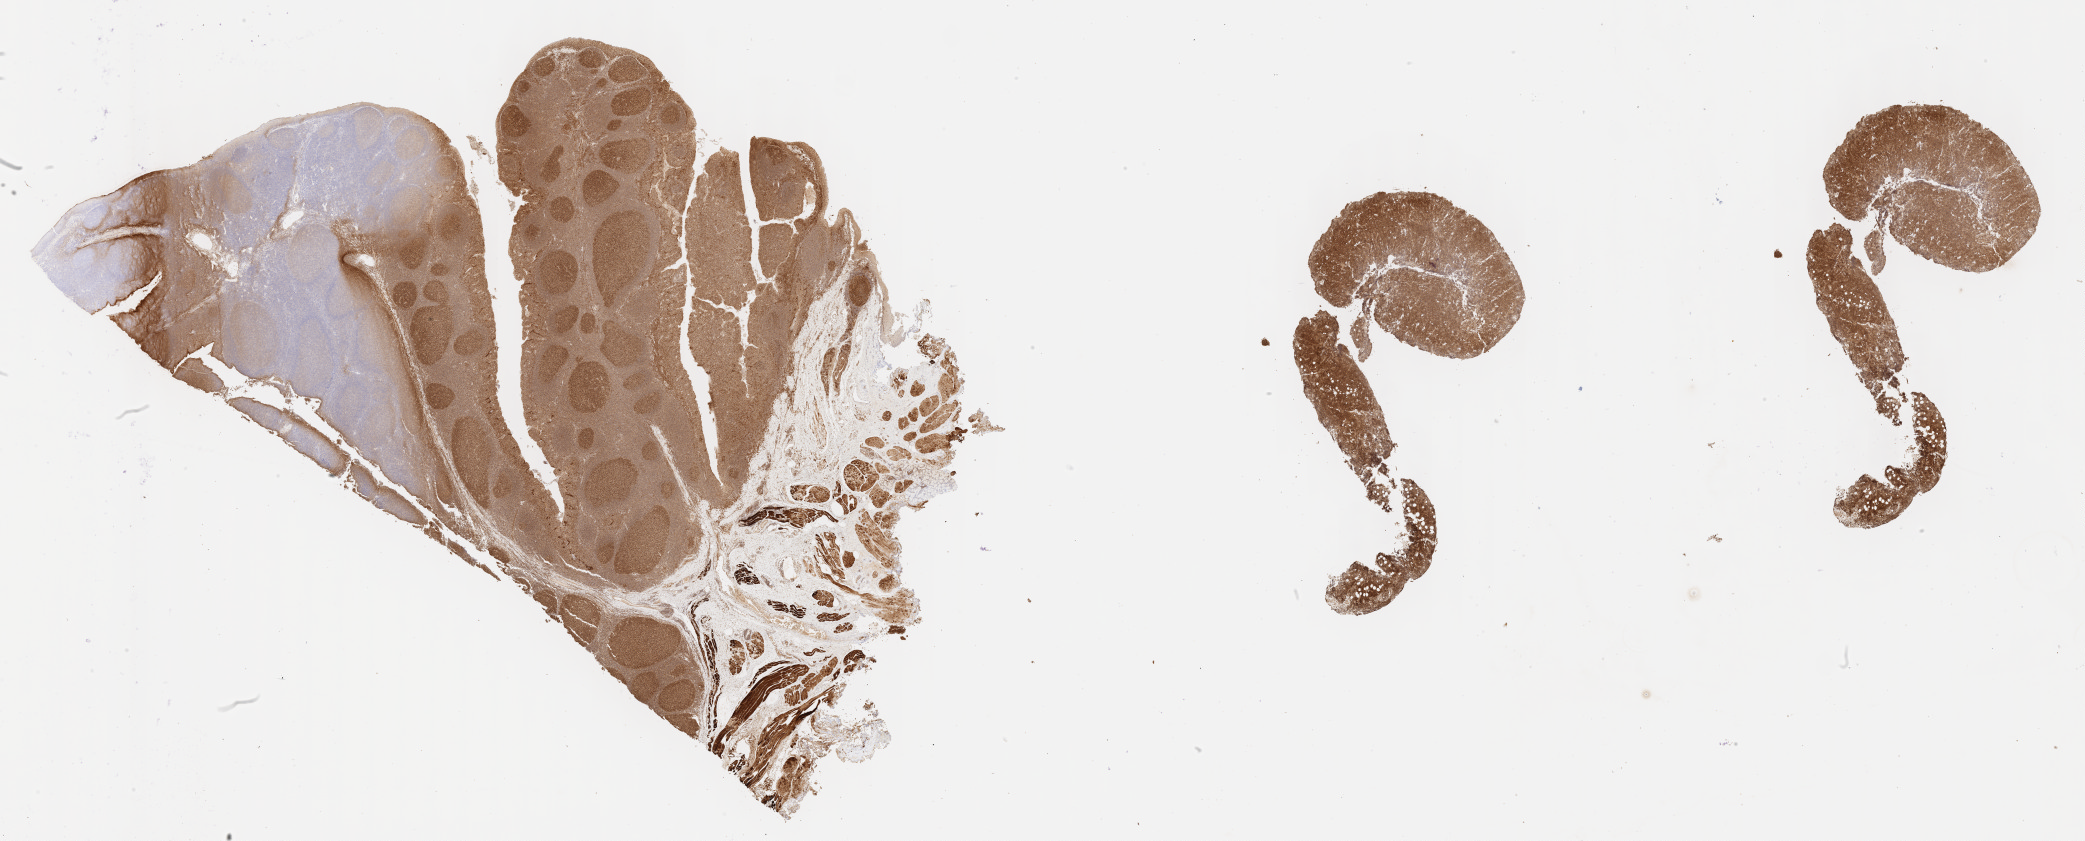
Immunohistochemistry (IHC) whole-slide image stained for BCL6, low-resolution overview of the scanned area, about 33.7 x 13.6 mm; specimen: tumor tissue; site: head and neck. Patient: female, age 55 years.
* diagnosis: Burkitt lymphoma, NOS